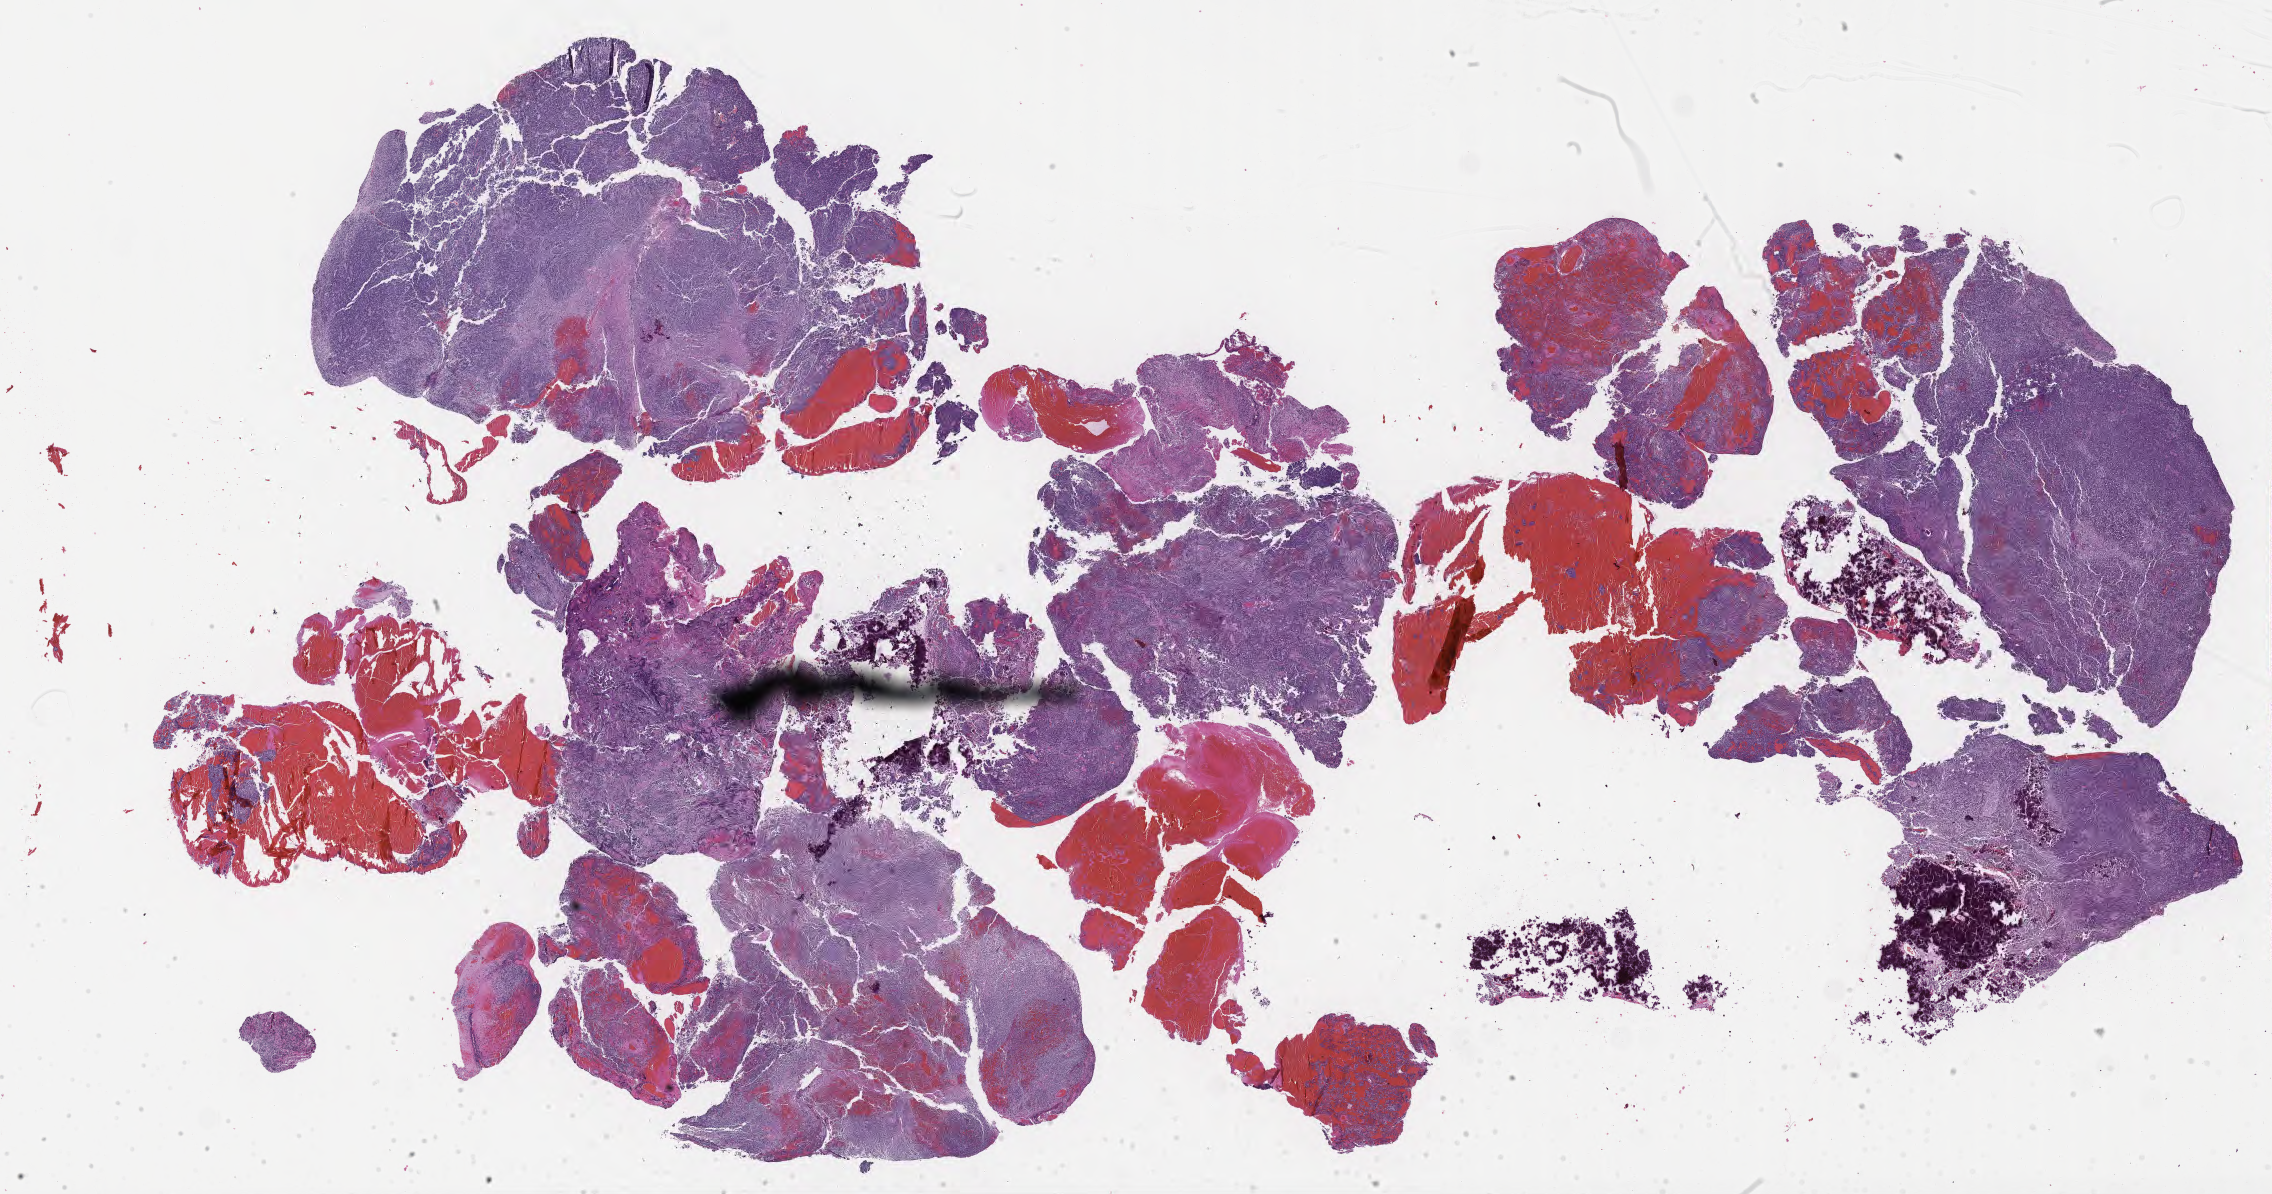
Digitized haematoxylin and eosin-stained section of tumor tissue from the cerebellum — a low-resolution overview of the entire scanned area, about 36.7 x 19.3 mm, FFPE section. Male patient, age 58 months (4 years 10 months).
Diagnosis: Medulloblastoma, NOS.